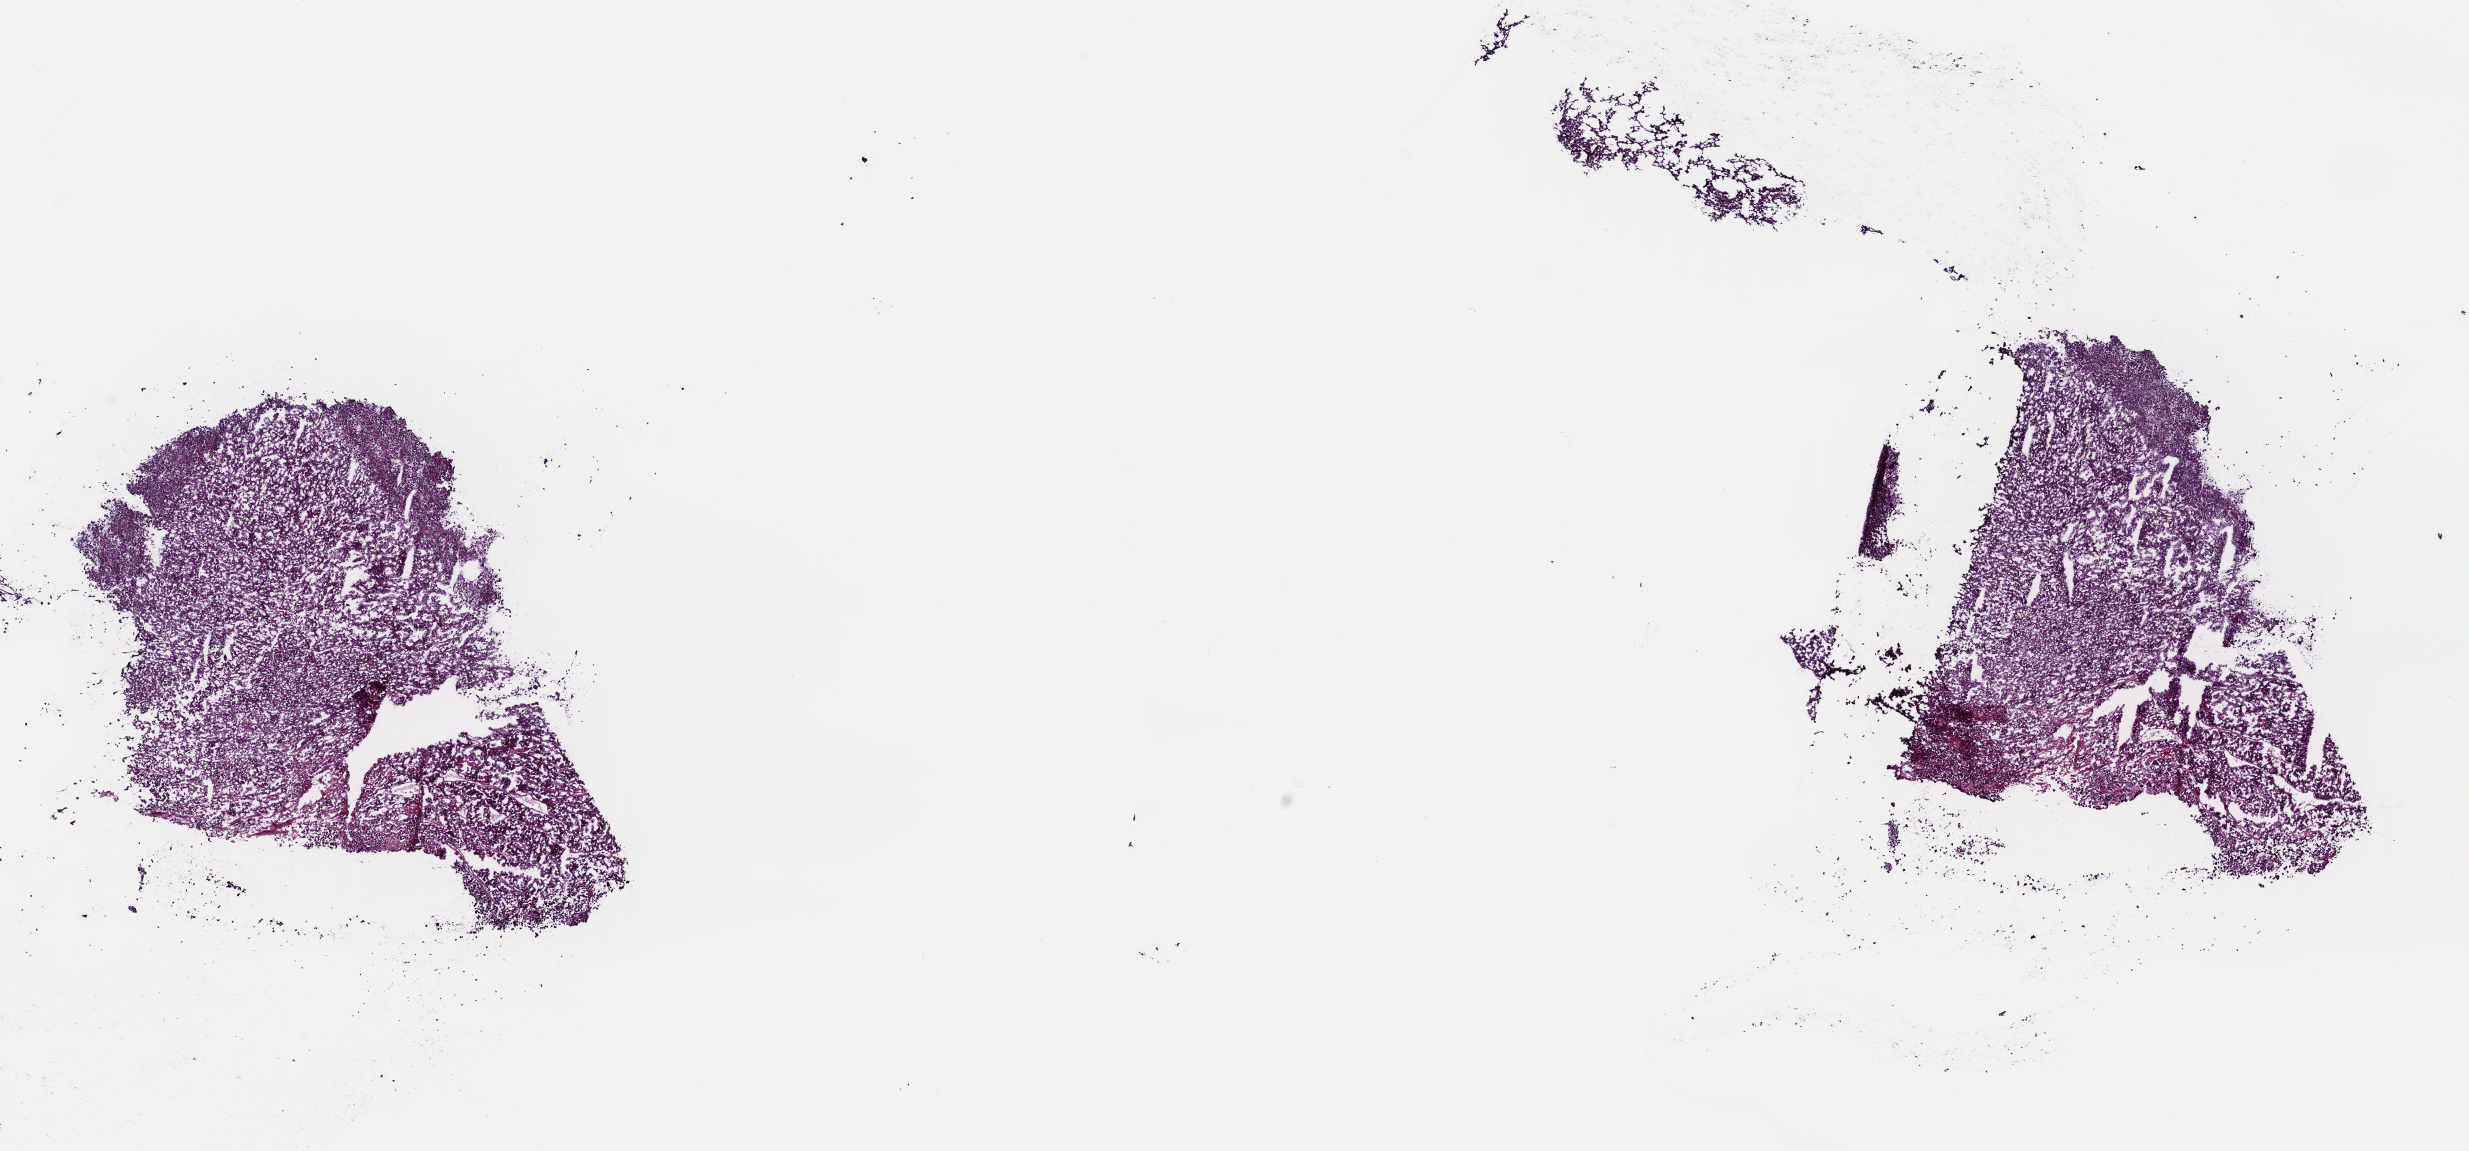
H&E-stained whole-slide image, shown as a low-resolution overview of the whole scanned area (about 19.5 x 9.1 mm), frozen section, primary tumour sample from the adrenal cortex. Female patient; age at initial diagnosis 32 years. Pathologist review of this section (percent, as recorded): tumour cells 95%, tumour nuclei 100%, normal cells 0%, stromal cells 5%, necrosis 0%. Inflammatory infiltration, as recorded: lymphocyte infiltration 0%, monocyte infiltration 0%, neutrophil infiltration 0%.
Lymph nodes positive (case pathology): 0 of 1 examined. Diagnosis: Adrenal cortical carcinoma (cortex of adrenal gland).